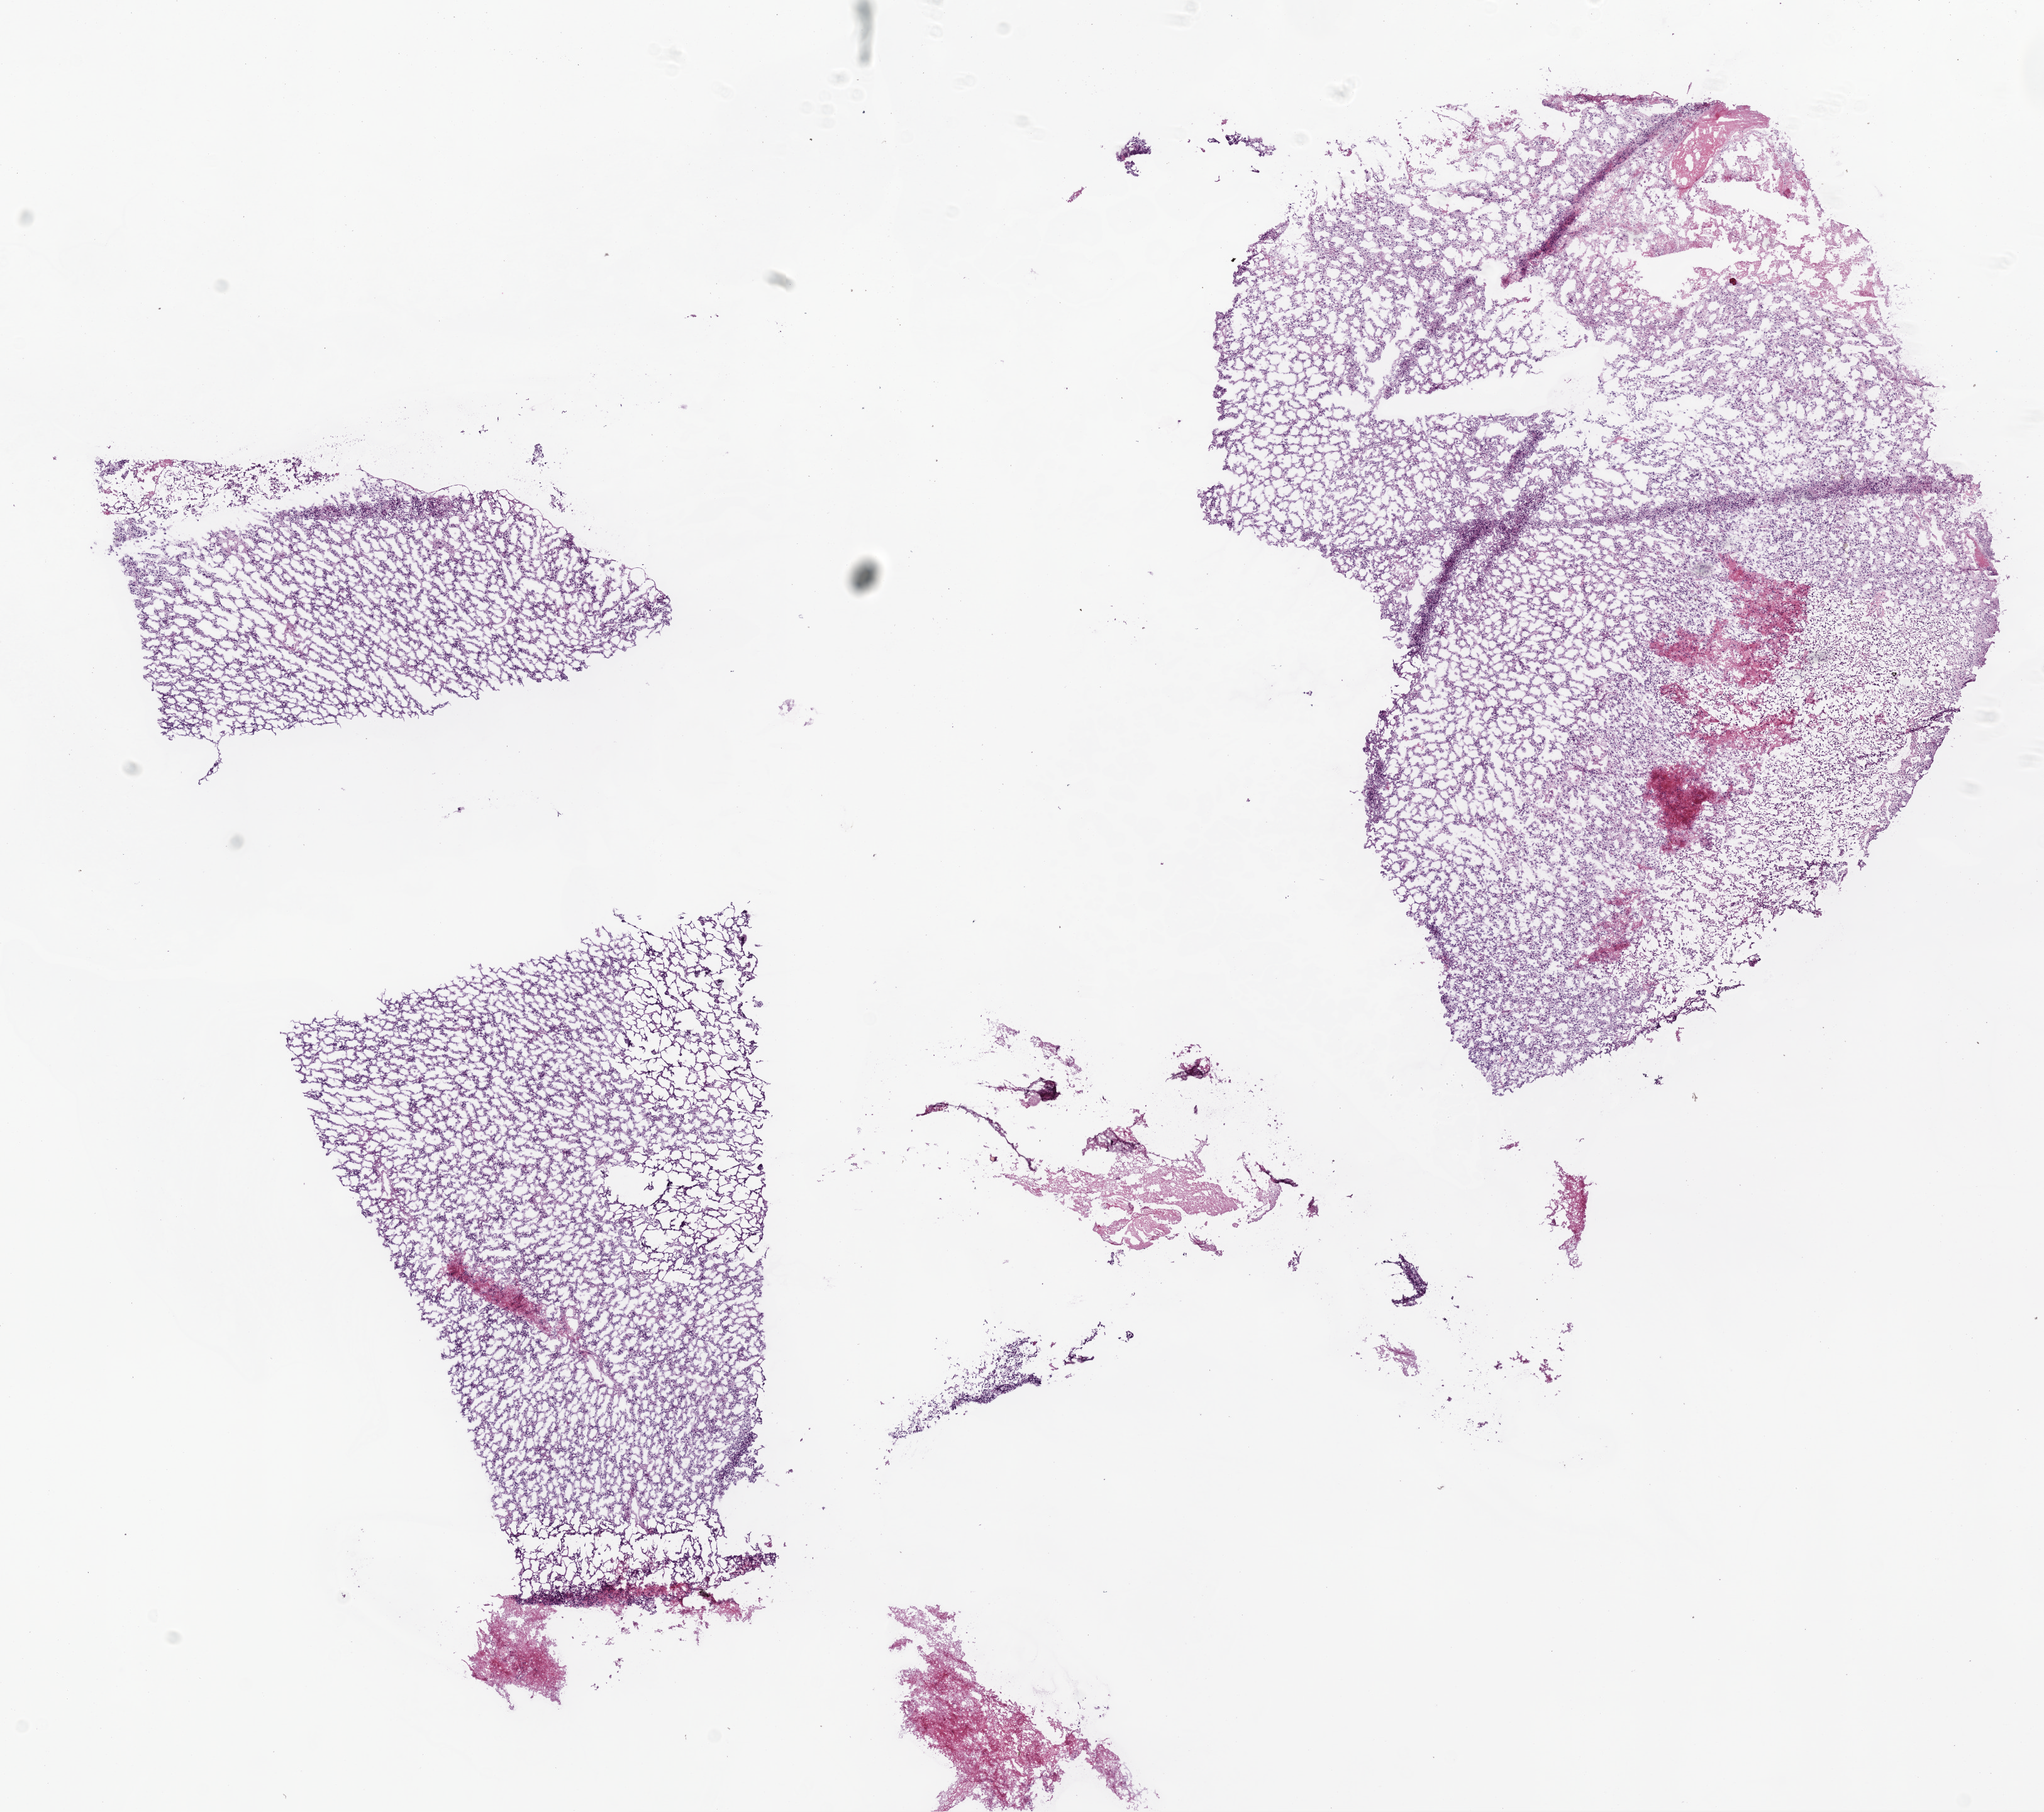
Digitized H&E tissue section (whole slide) — shown as a low-resolution overview of the whole scanned area (about 13.0 x 11.6 mm); frozen section from the bottom of the tissue portion; primary tumour sample from the brain. Patient: female, age at initial diagnosis 67 years.
Pathologic diagnosis: Glioblastoma.